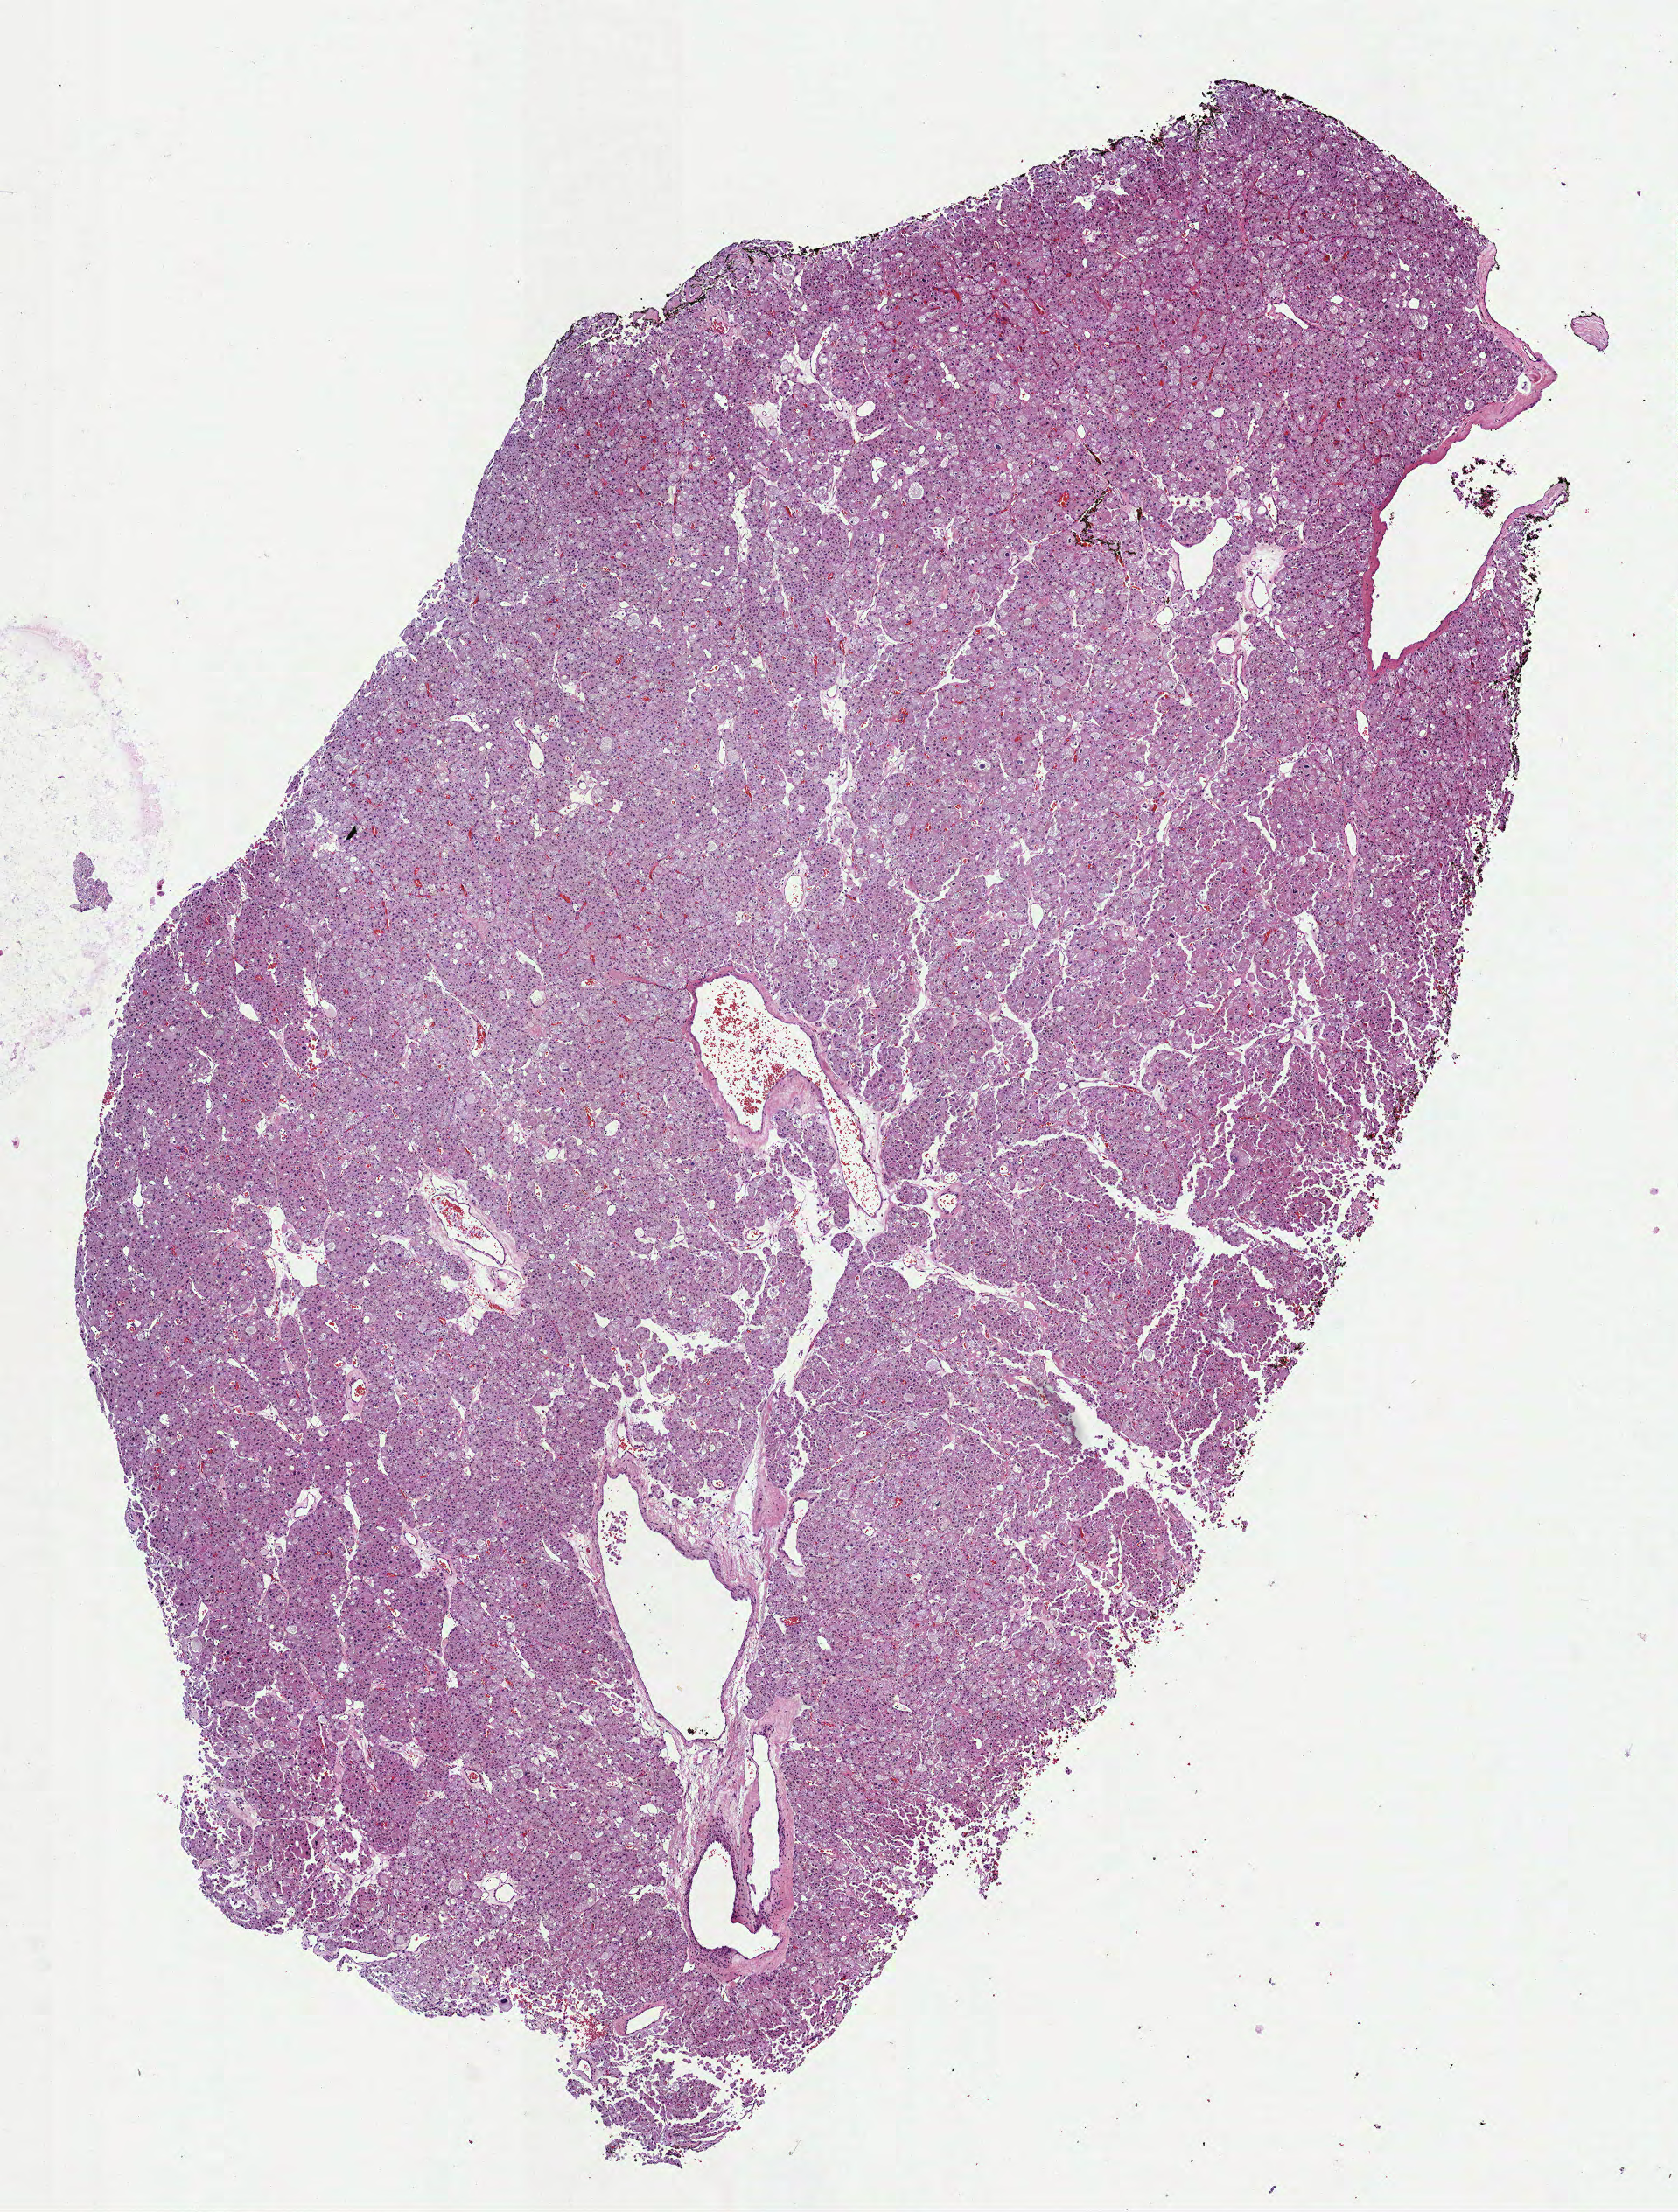
Digitized H&E-stained tissue section (whole slide) — shown as a low-resolution overview of the whole scanned area (about 7.7 x 10.2 mm). Formalin-fixed paraffin-embedded (FFPE) diagnostic section. Kidney, primary tumour sample. Female, age 40 years at initial diagnosis.
* histologic diagnosis: Renal cell carcinoma, chromophobe type
* TNM: T2b NX MX
* AJCC pathologic stage: II (7th edition)